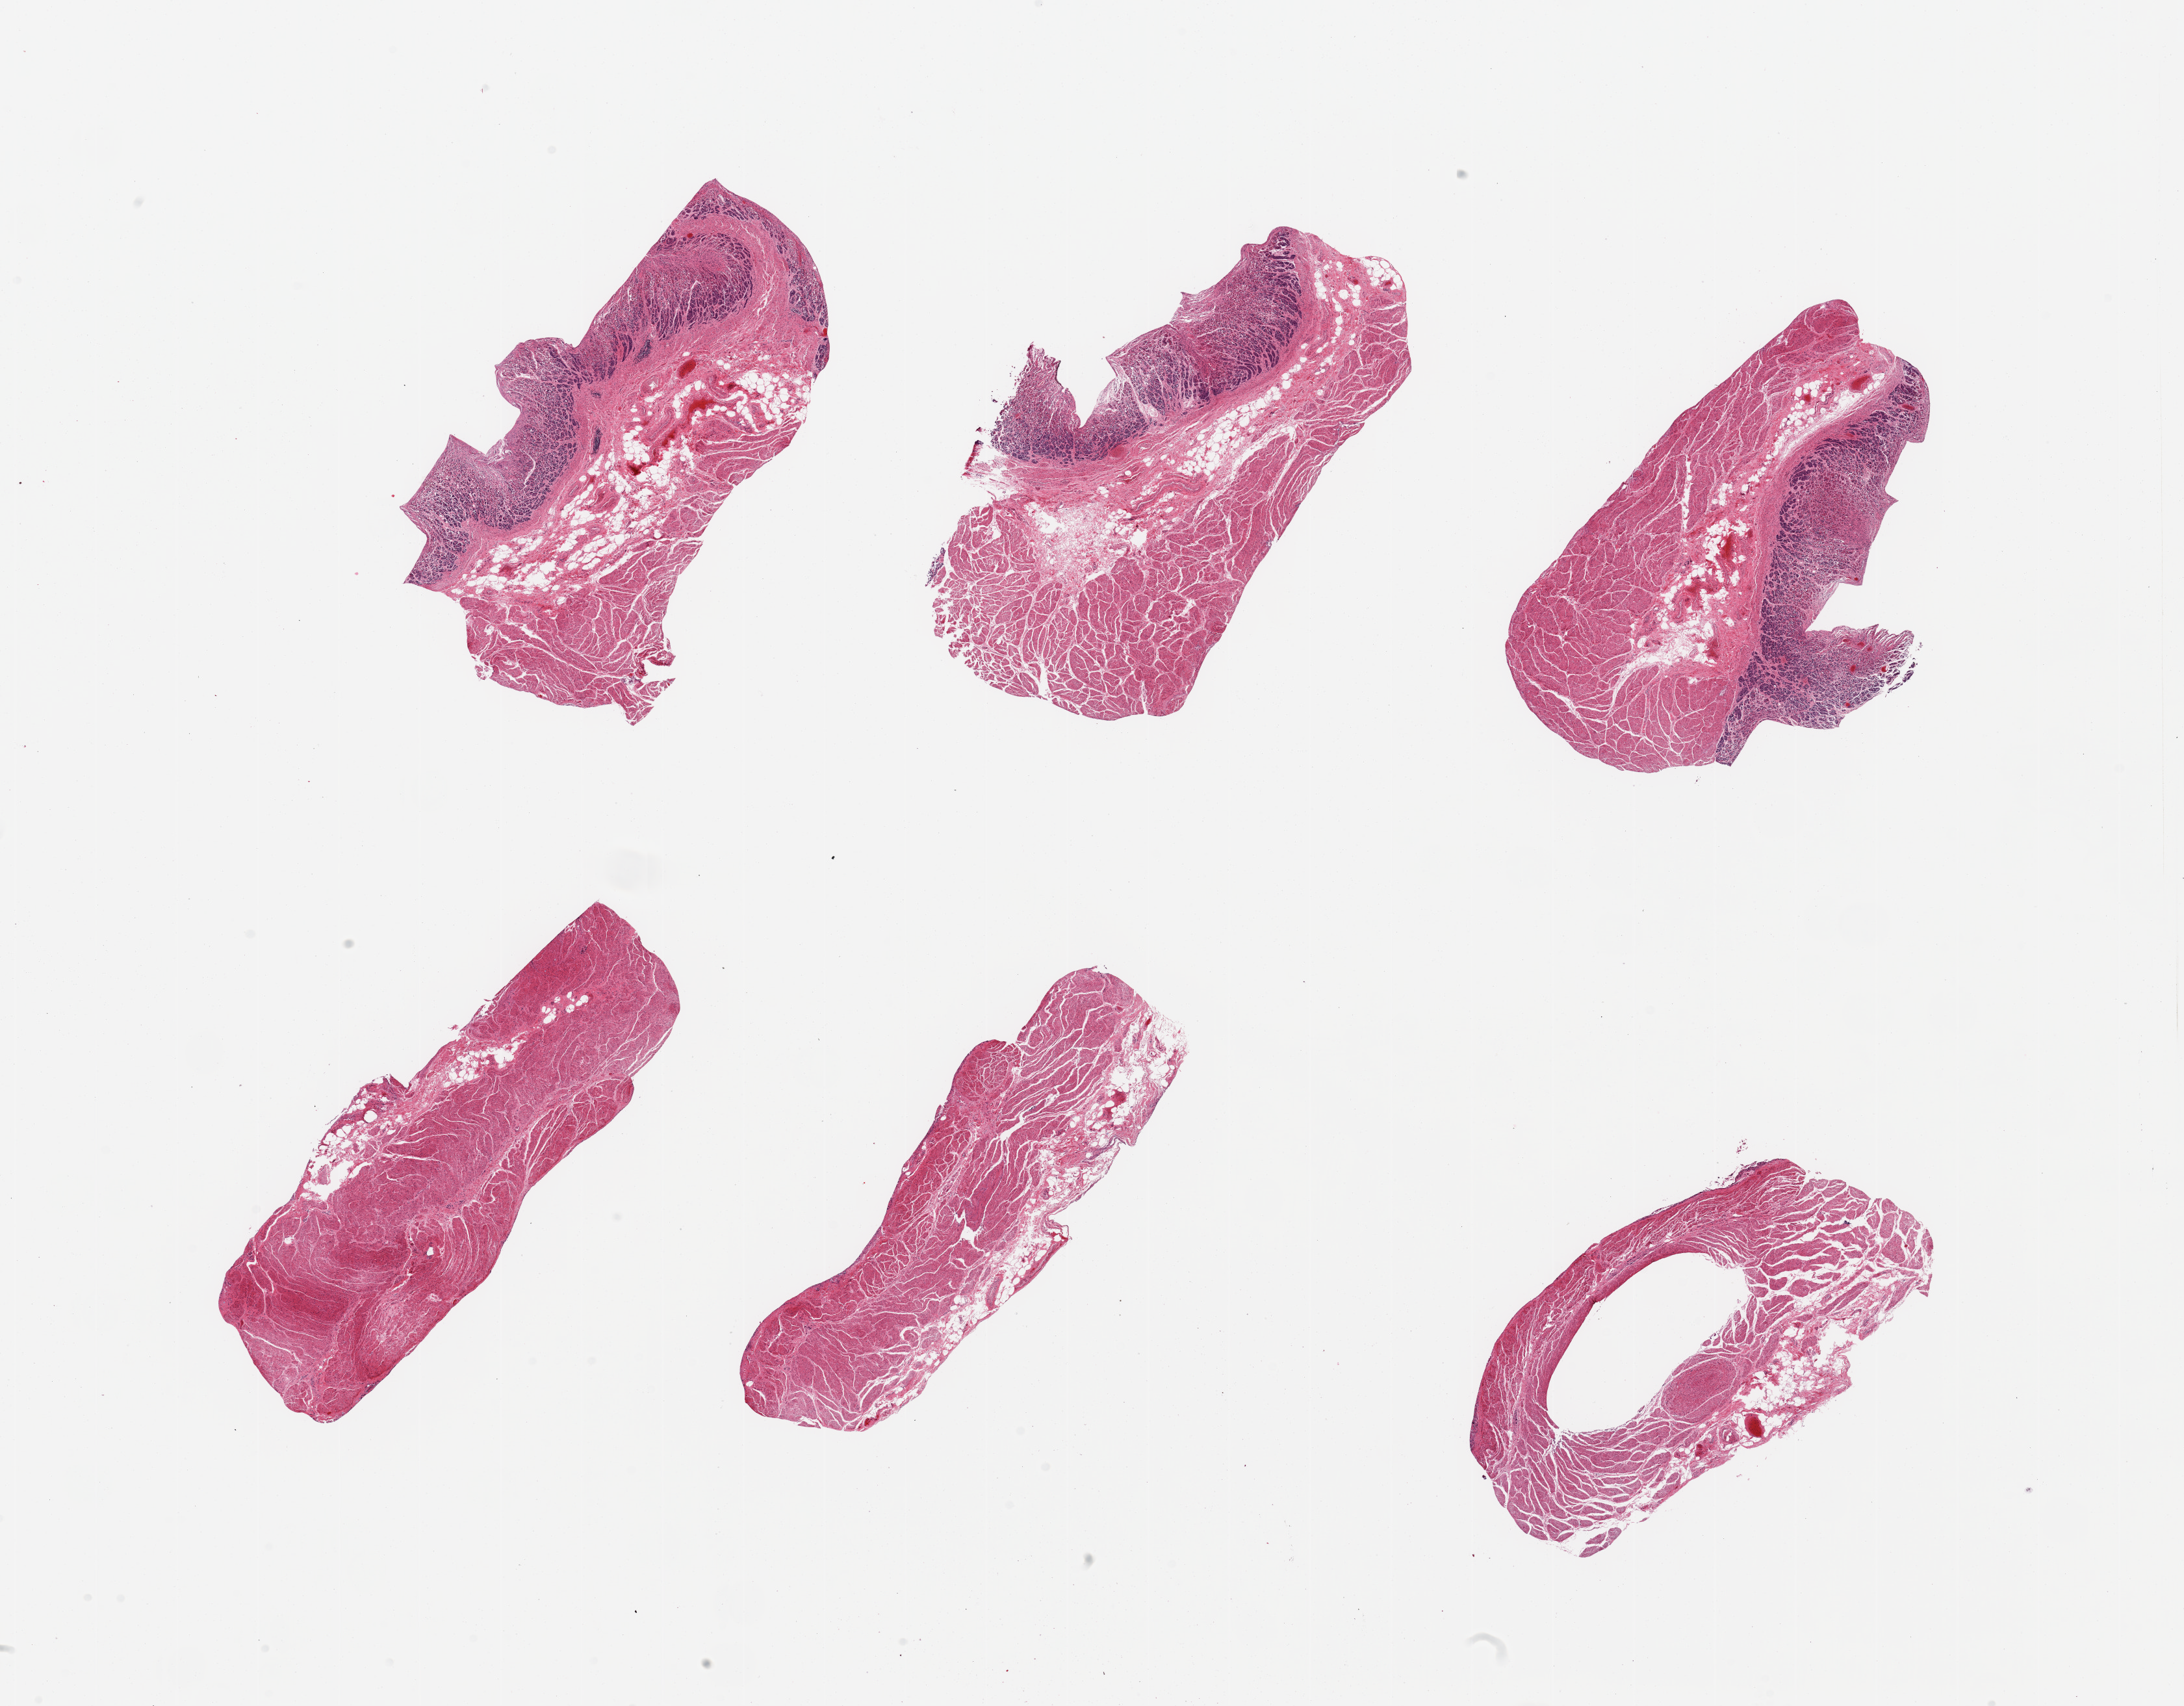
Whole-slide image, H&E stain, low-resolution overview of the scanned area, about 26.6 x 20.8 mm (acquisition: 20x scan). PAXgene-fixed, paraffin-embedded tissue. Target tissue: gastroesophageal junction. Donor tissue sample.
- pathologist's review note for this sample: 6 pieces, 3 pieces include gastric mucosa